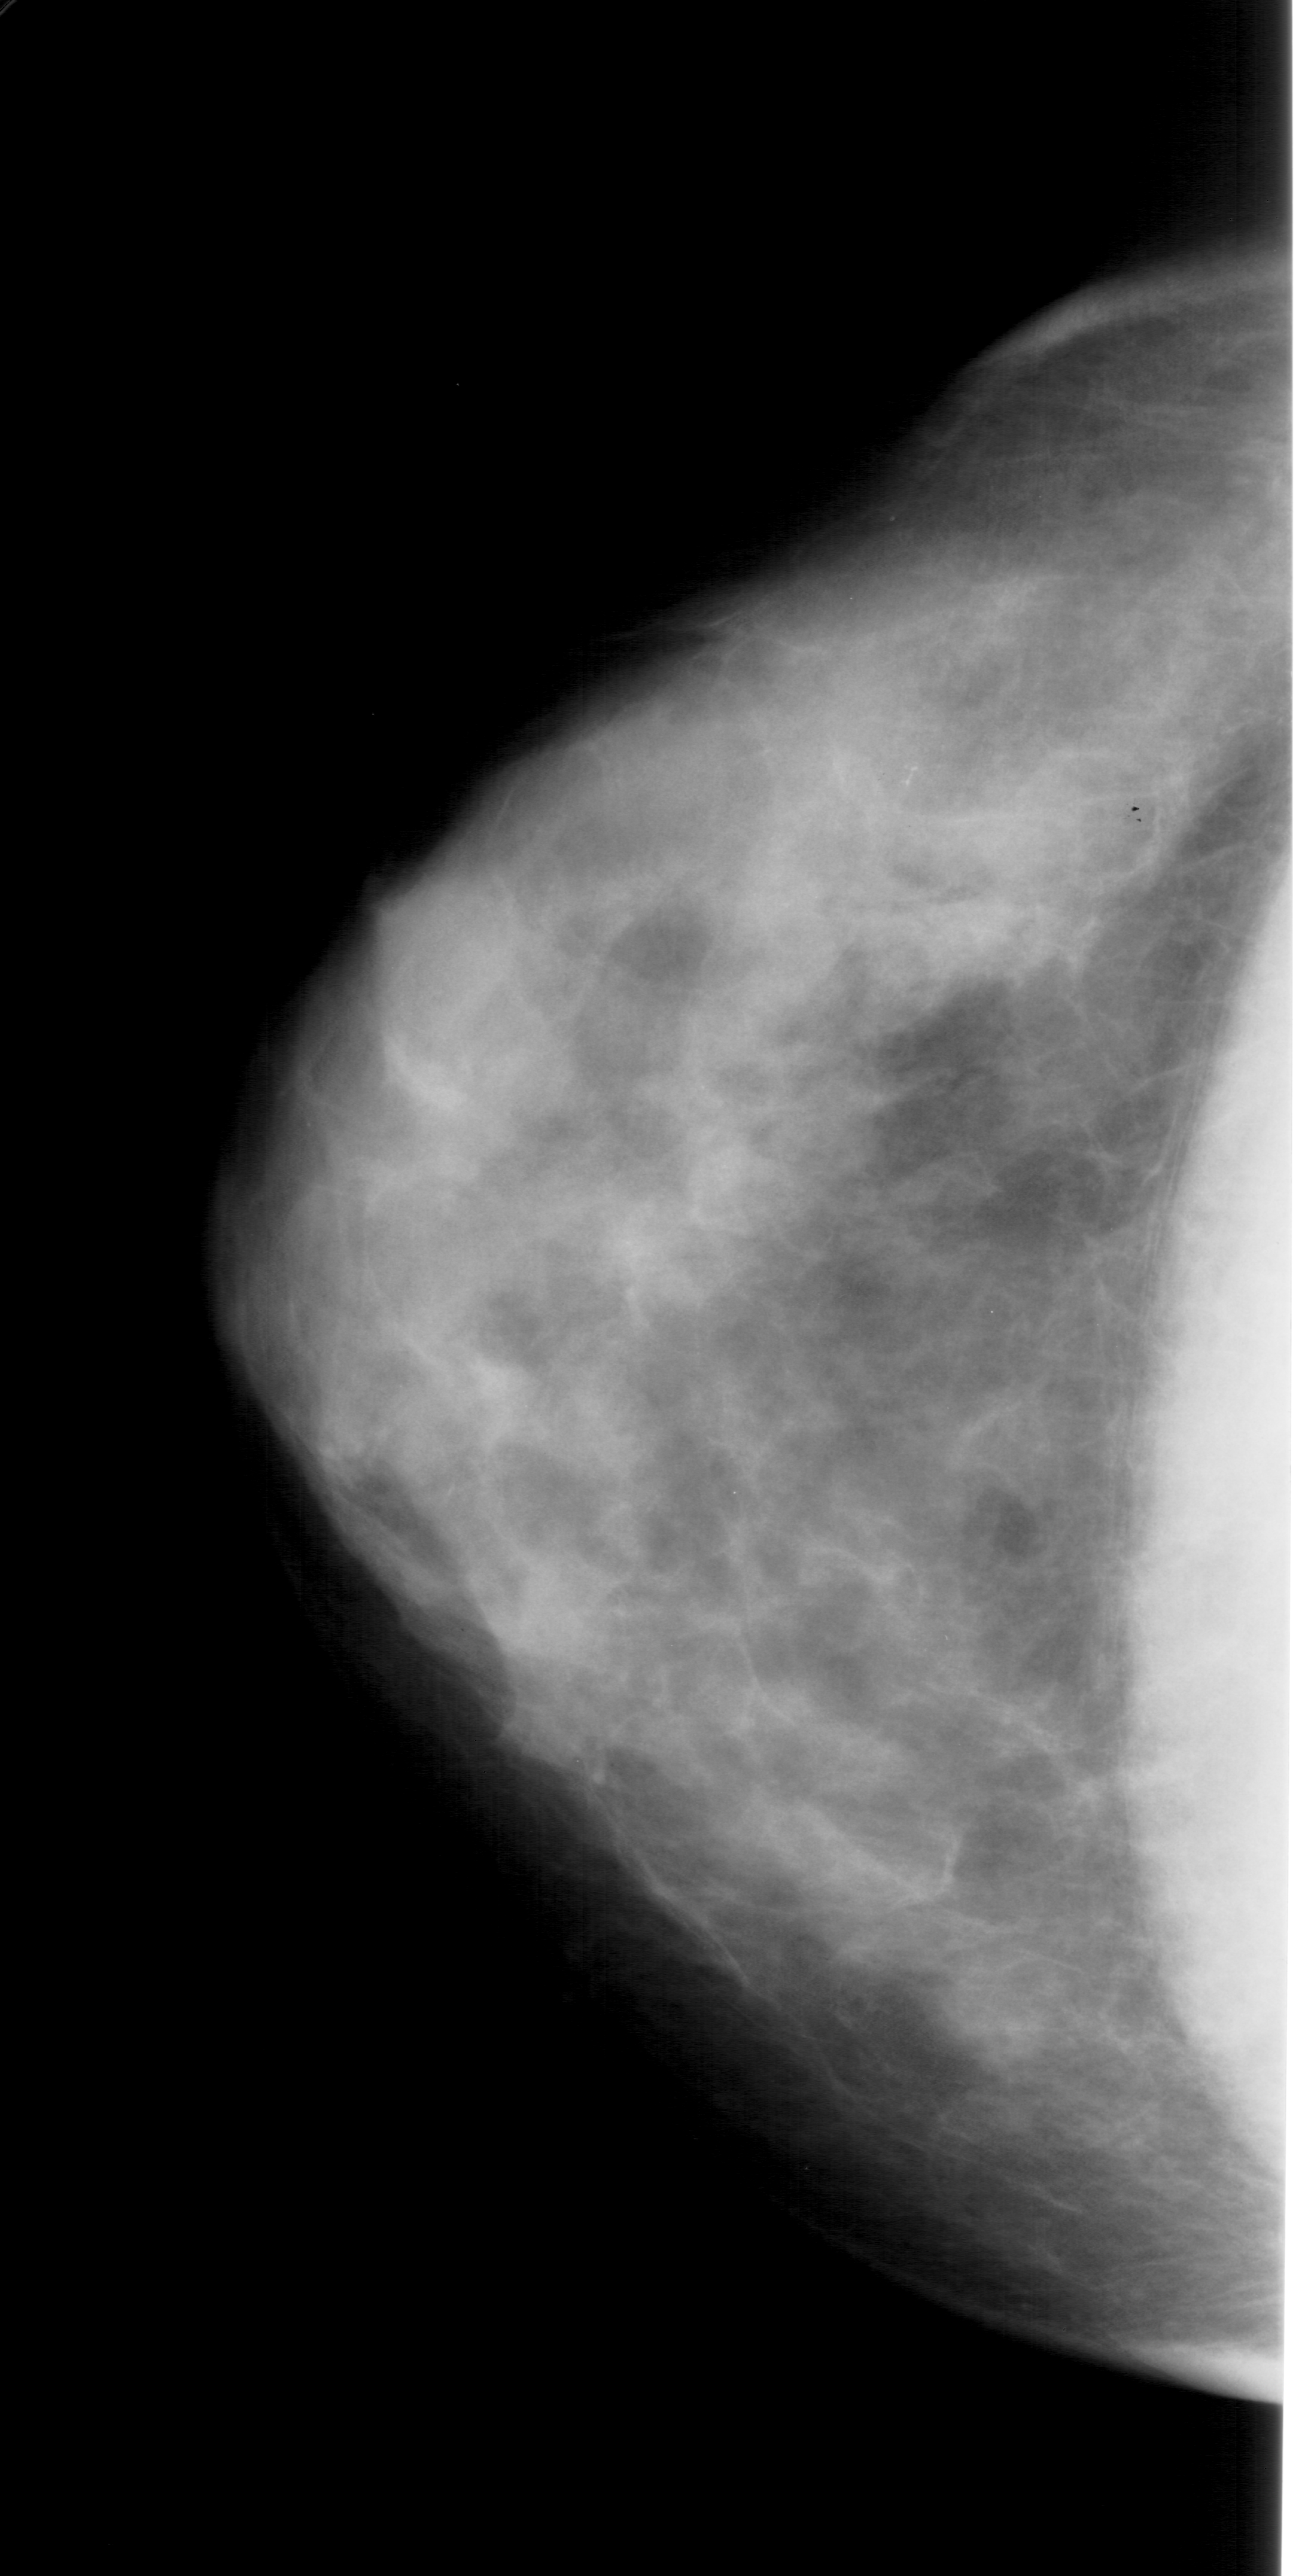
Mammogram (digitized film); left breast; CC view; breast composition: extremely dense (BI-RADS density category 4 of 4).
Calcifications, morphology pleomorphic, distribution clustered; BI-RADS assessment category 4; pathology (as recorded): benign.